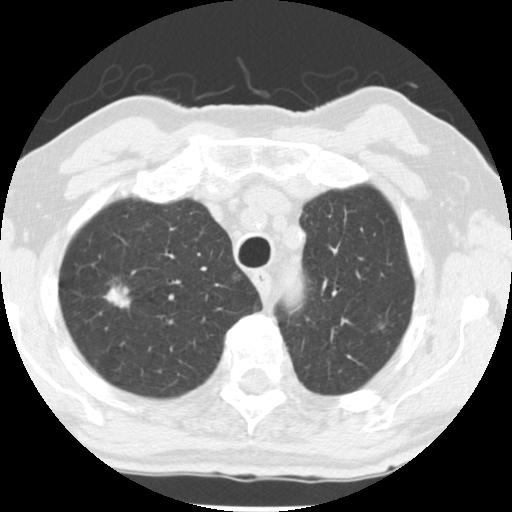
Chest CT (low-dose screening protocol), one axial image, first (baseline) screen, lung window (W 1500 / L -600 HU), 2.5 mm slice thickness, standard (soft-tissue) reconstruction kernel (STANDARD), 120 kVp, slice 206 of 252 in the series, 512 × 512 image matrix, field of view 313 × 313 mm. Male, age 69 years at enrolment.
Expert-annotated lung lesion, box from (x=90, y=271) to (x=148, y=329) px. The screening reader recorded 2 non-calcified nodules or masses ≥4 mm on this exam (right upper lobe, left upper lobe); which of them this box marks is not recorded. Participant outcome: lung cancer diagnosed 105 days after this screen — adenocarcinoma, NOS, right upper lobe, well differentiated (G1), stage IA (AJCC 6th edition), 17 mm at pathology.